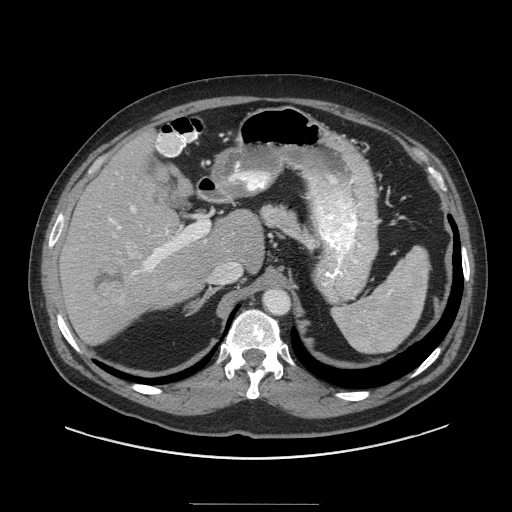
Contrast-enhanced abdominal CT (liver protocol), one axial slice. Position 62 of 91 along the scan axis. 140 kVp. Soft-tissue window (W 400 / L 40 HU). 2.5 mm slice thickness. 512 × 512 image matrix, field of view 440 × 440 mm. Case-level facts recorded for this patient, not image findings: diagnosis: hepatocellular carcinoma (patient treated with transarterial chemoembolisation; whether this scan precedes or follows treatment is not stated here); TNM stage (as recorded): Stage-I; Child-Pugh class: A; tumour nodularity: uninodular; tumour size: 4 cm.
Outlined on this slice (semi-automatic segmentation, software-assisted and operator-edited):
- liver parenchyma outside the tumour (the mass and vessels are separate outlines, so this box may not span the whole liver): bounding box <58,132,264,344> (left, top, right, bottom; pixels)
- mass: <91,260,128,299>
- liver vessels: <109,206,242,280>